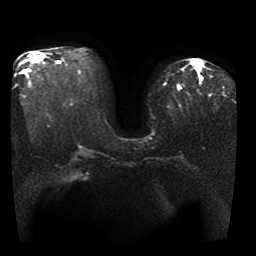
Breast MRI, one axial slice. Diffusion-weighted series; image 2 of 4 stored at this slice position (different b-values; order by instance number). 1.5 T. 256 × 256 image matrix, field of view 330 × 330 mm. Female patient.
Outlined on this slice (manually delineated by an expert):
- tumour on diffusion-weighted imaging: box from (x=200, y=77) to (x=202, y=80) px